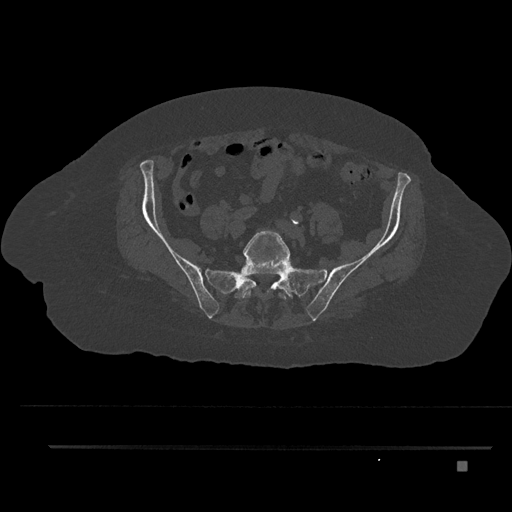
CT including the spine, one axial slice; position 18 of 797 along the scan axis; 120 kVp; bone window (W 1800 / L 400 HU); 0.5 mm slice thickness; 512 × 512 image matrix, field of view 437 × 437 mm. Patient: female, 76 years. Case-level facts recorded for this patient, not image findings: primary cancer: lung; vertebrae with lytic lesions (as recorded): T11, L3.
Structures marked on this image (semi-automatically segmented with operator editing):
- L5 vertebra: bounding box (x1, y1, x2, y2) in pixels: (242, 230, 290, 300)